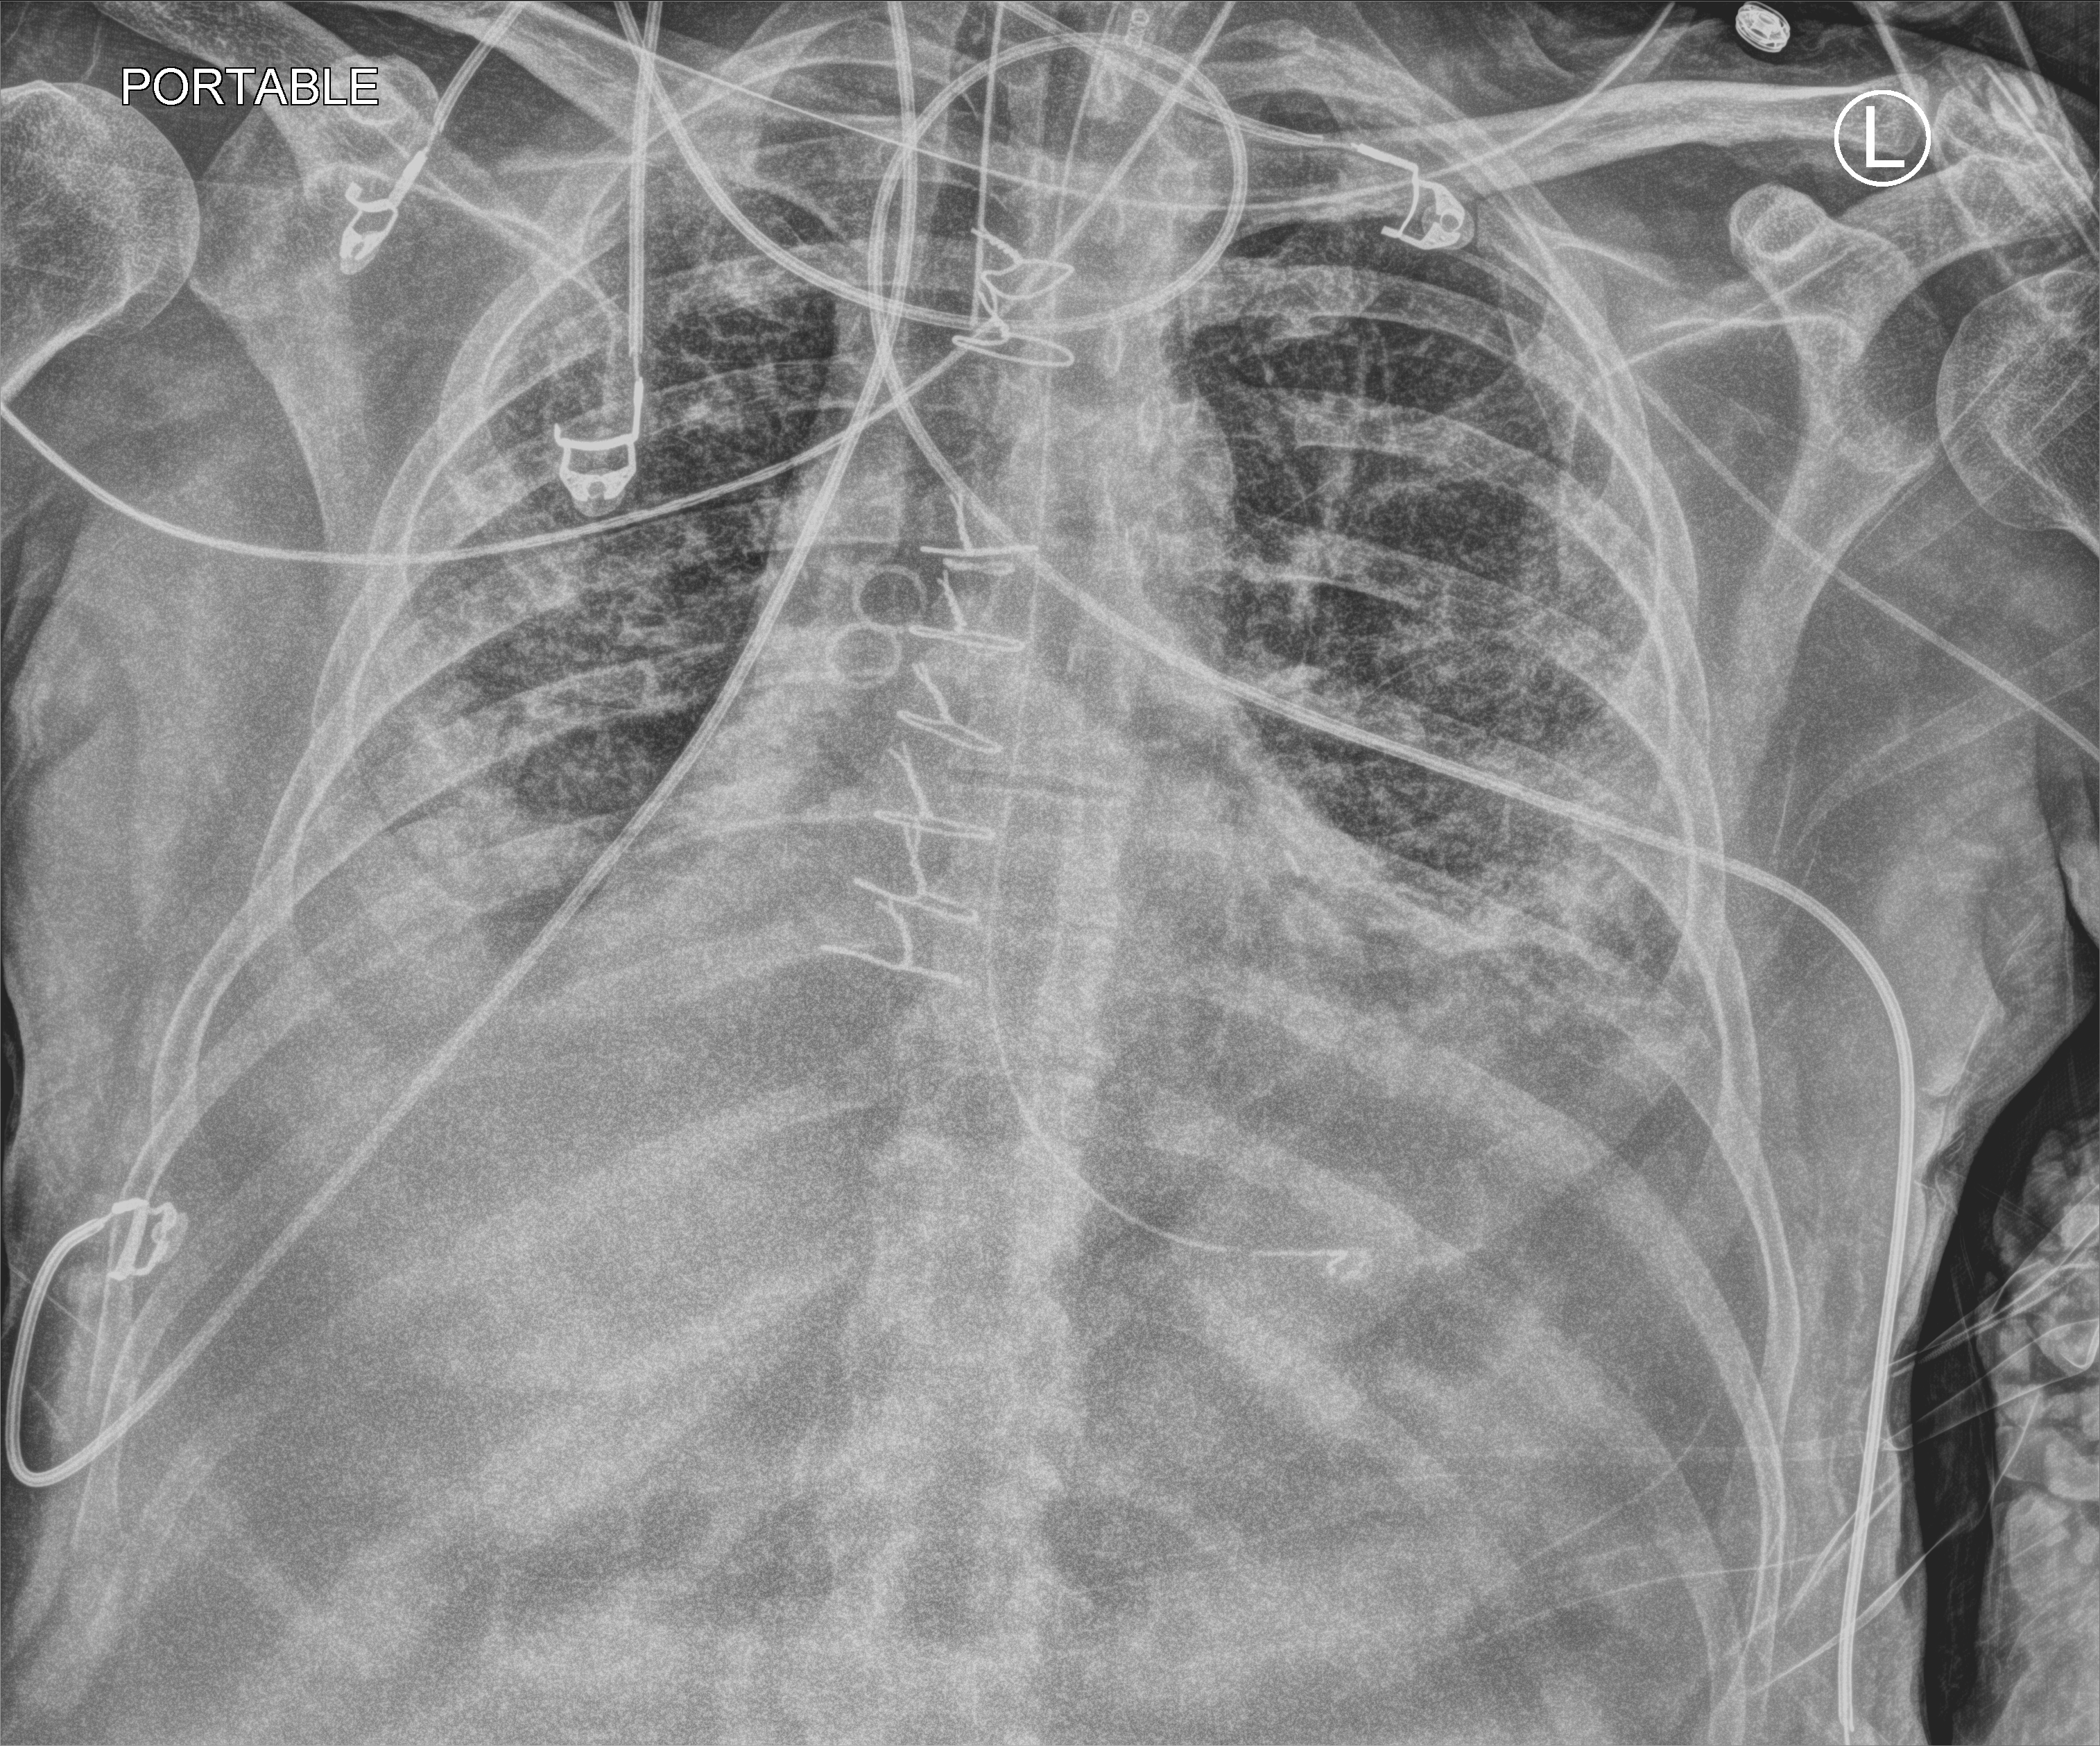
Portable chest radiograph; anteroposterior (AP) projection. Male patient hospitalised with COVID-19, age 18–59 years.
From the hospital-stay record, not from the radiograph (when in the stay this image was taken is not recorded):
- length of hospital stay: 63 days